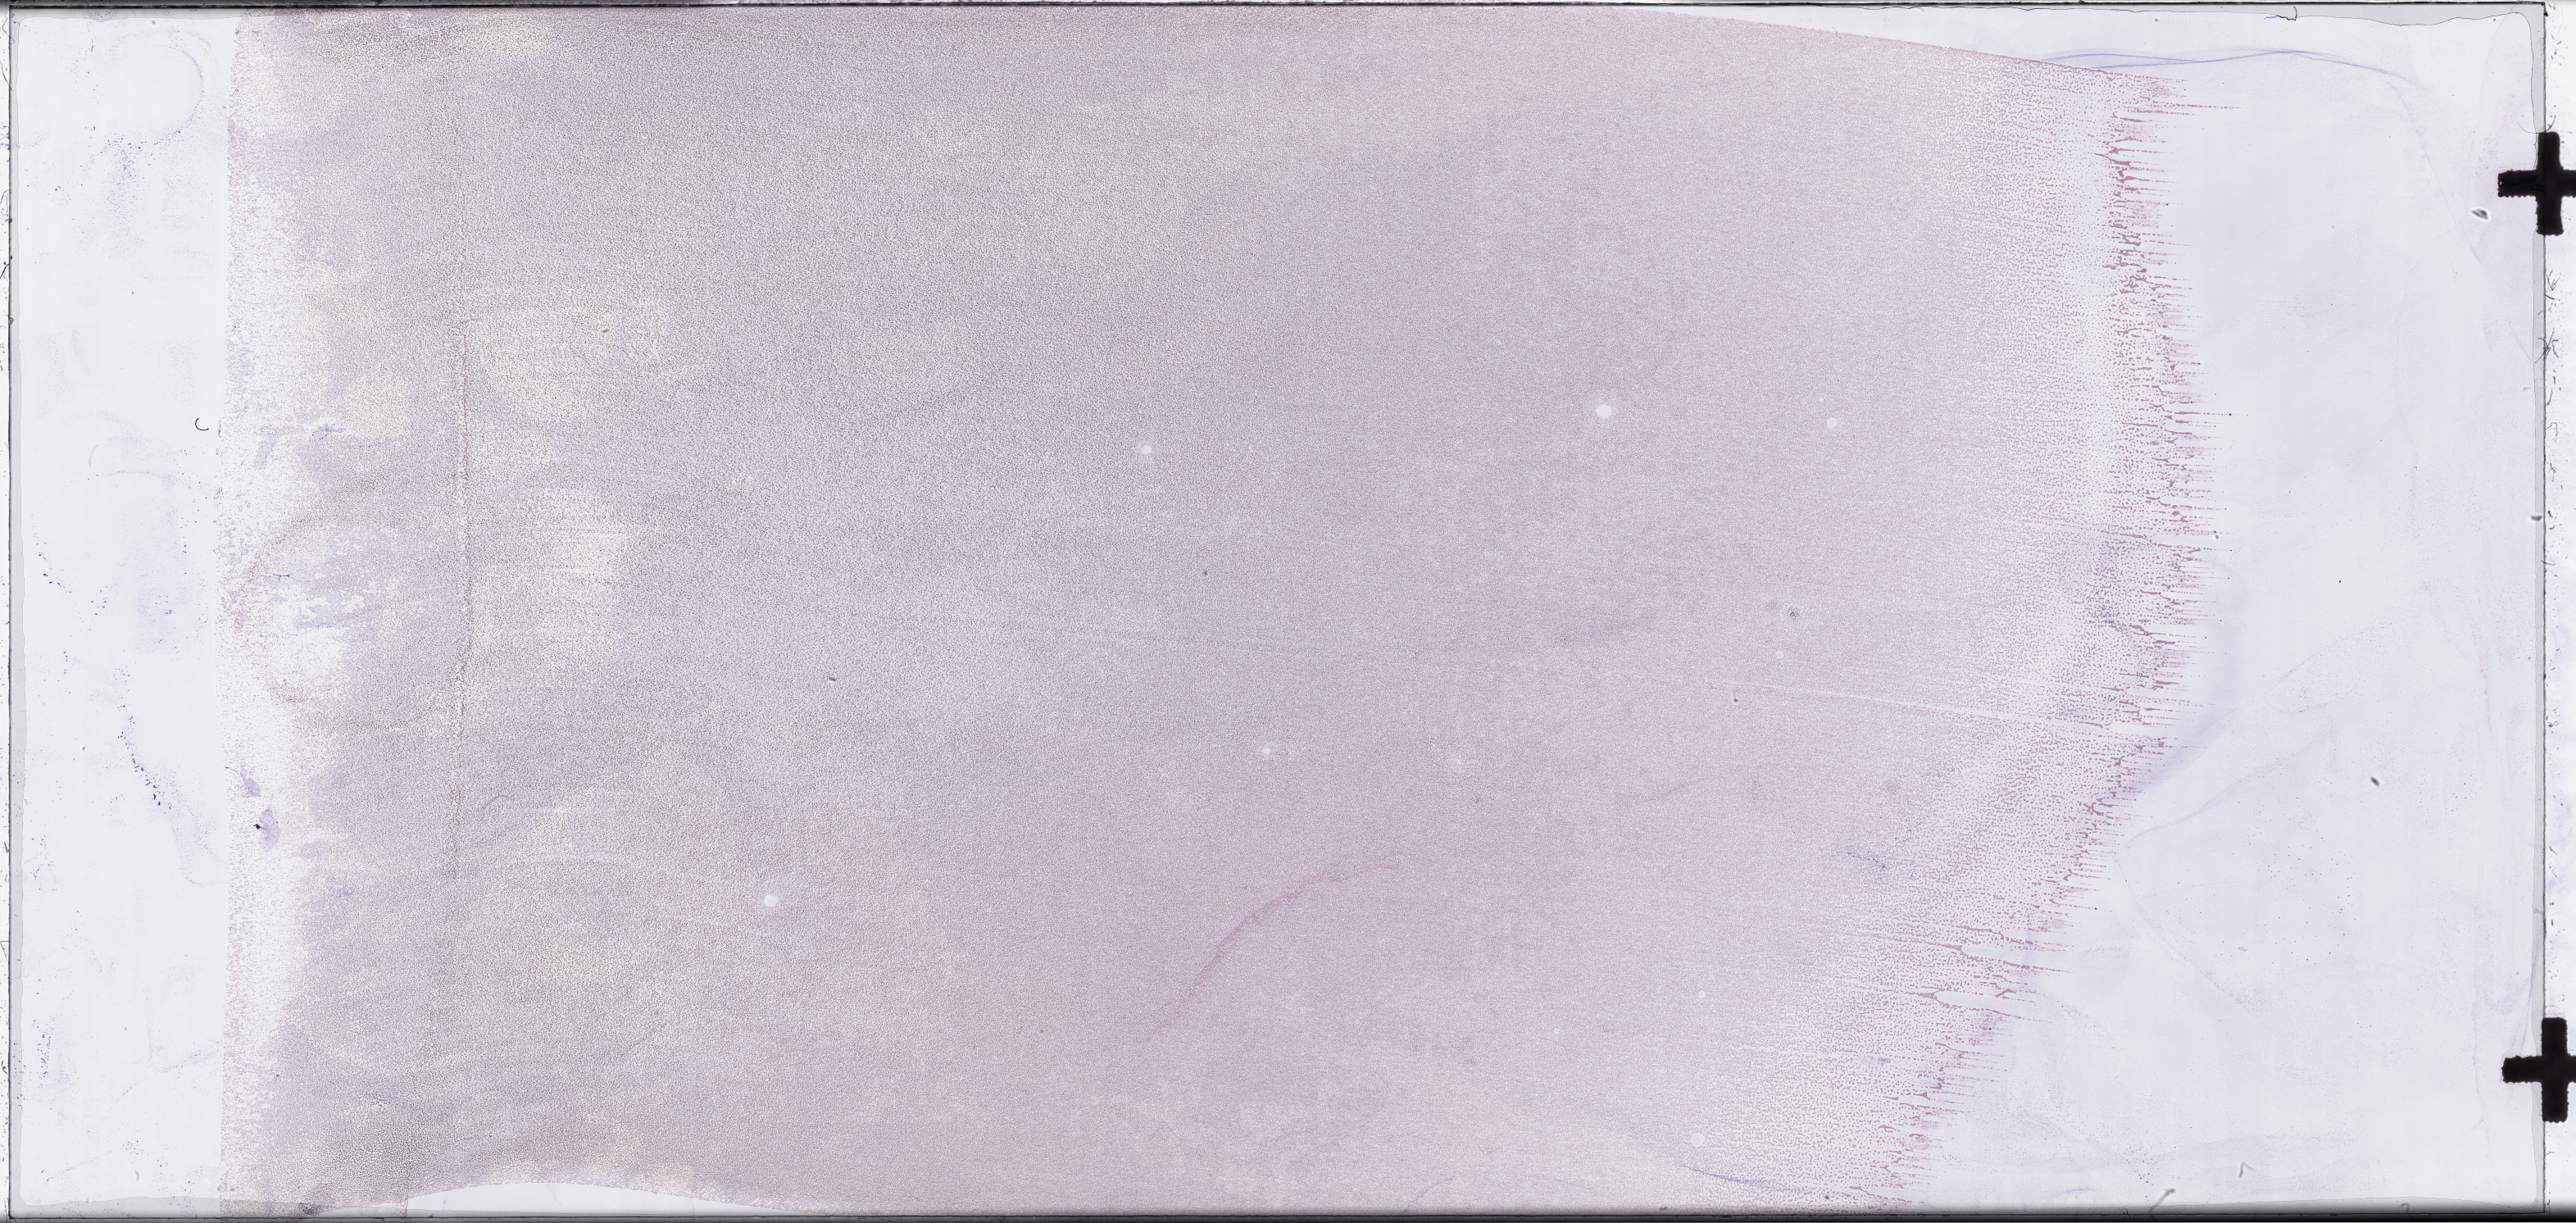
Whole-slide image of a bone marrow smear, Wright-Giemsa stain, shown as a low-resolution overview of the whole scanned area (about 50.8 x 24.1 mm). Smear from an EDTA sample. Specimen time point: collected at baseline (before treatment). Male patient.
From a patient with: Plasma Cell Myeloma.